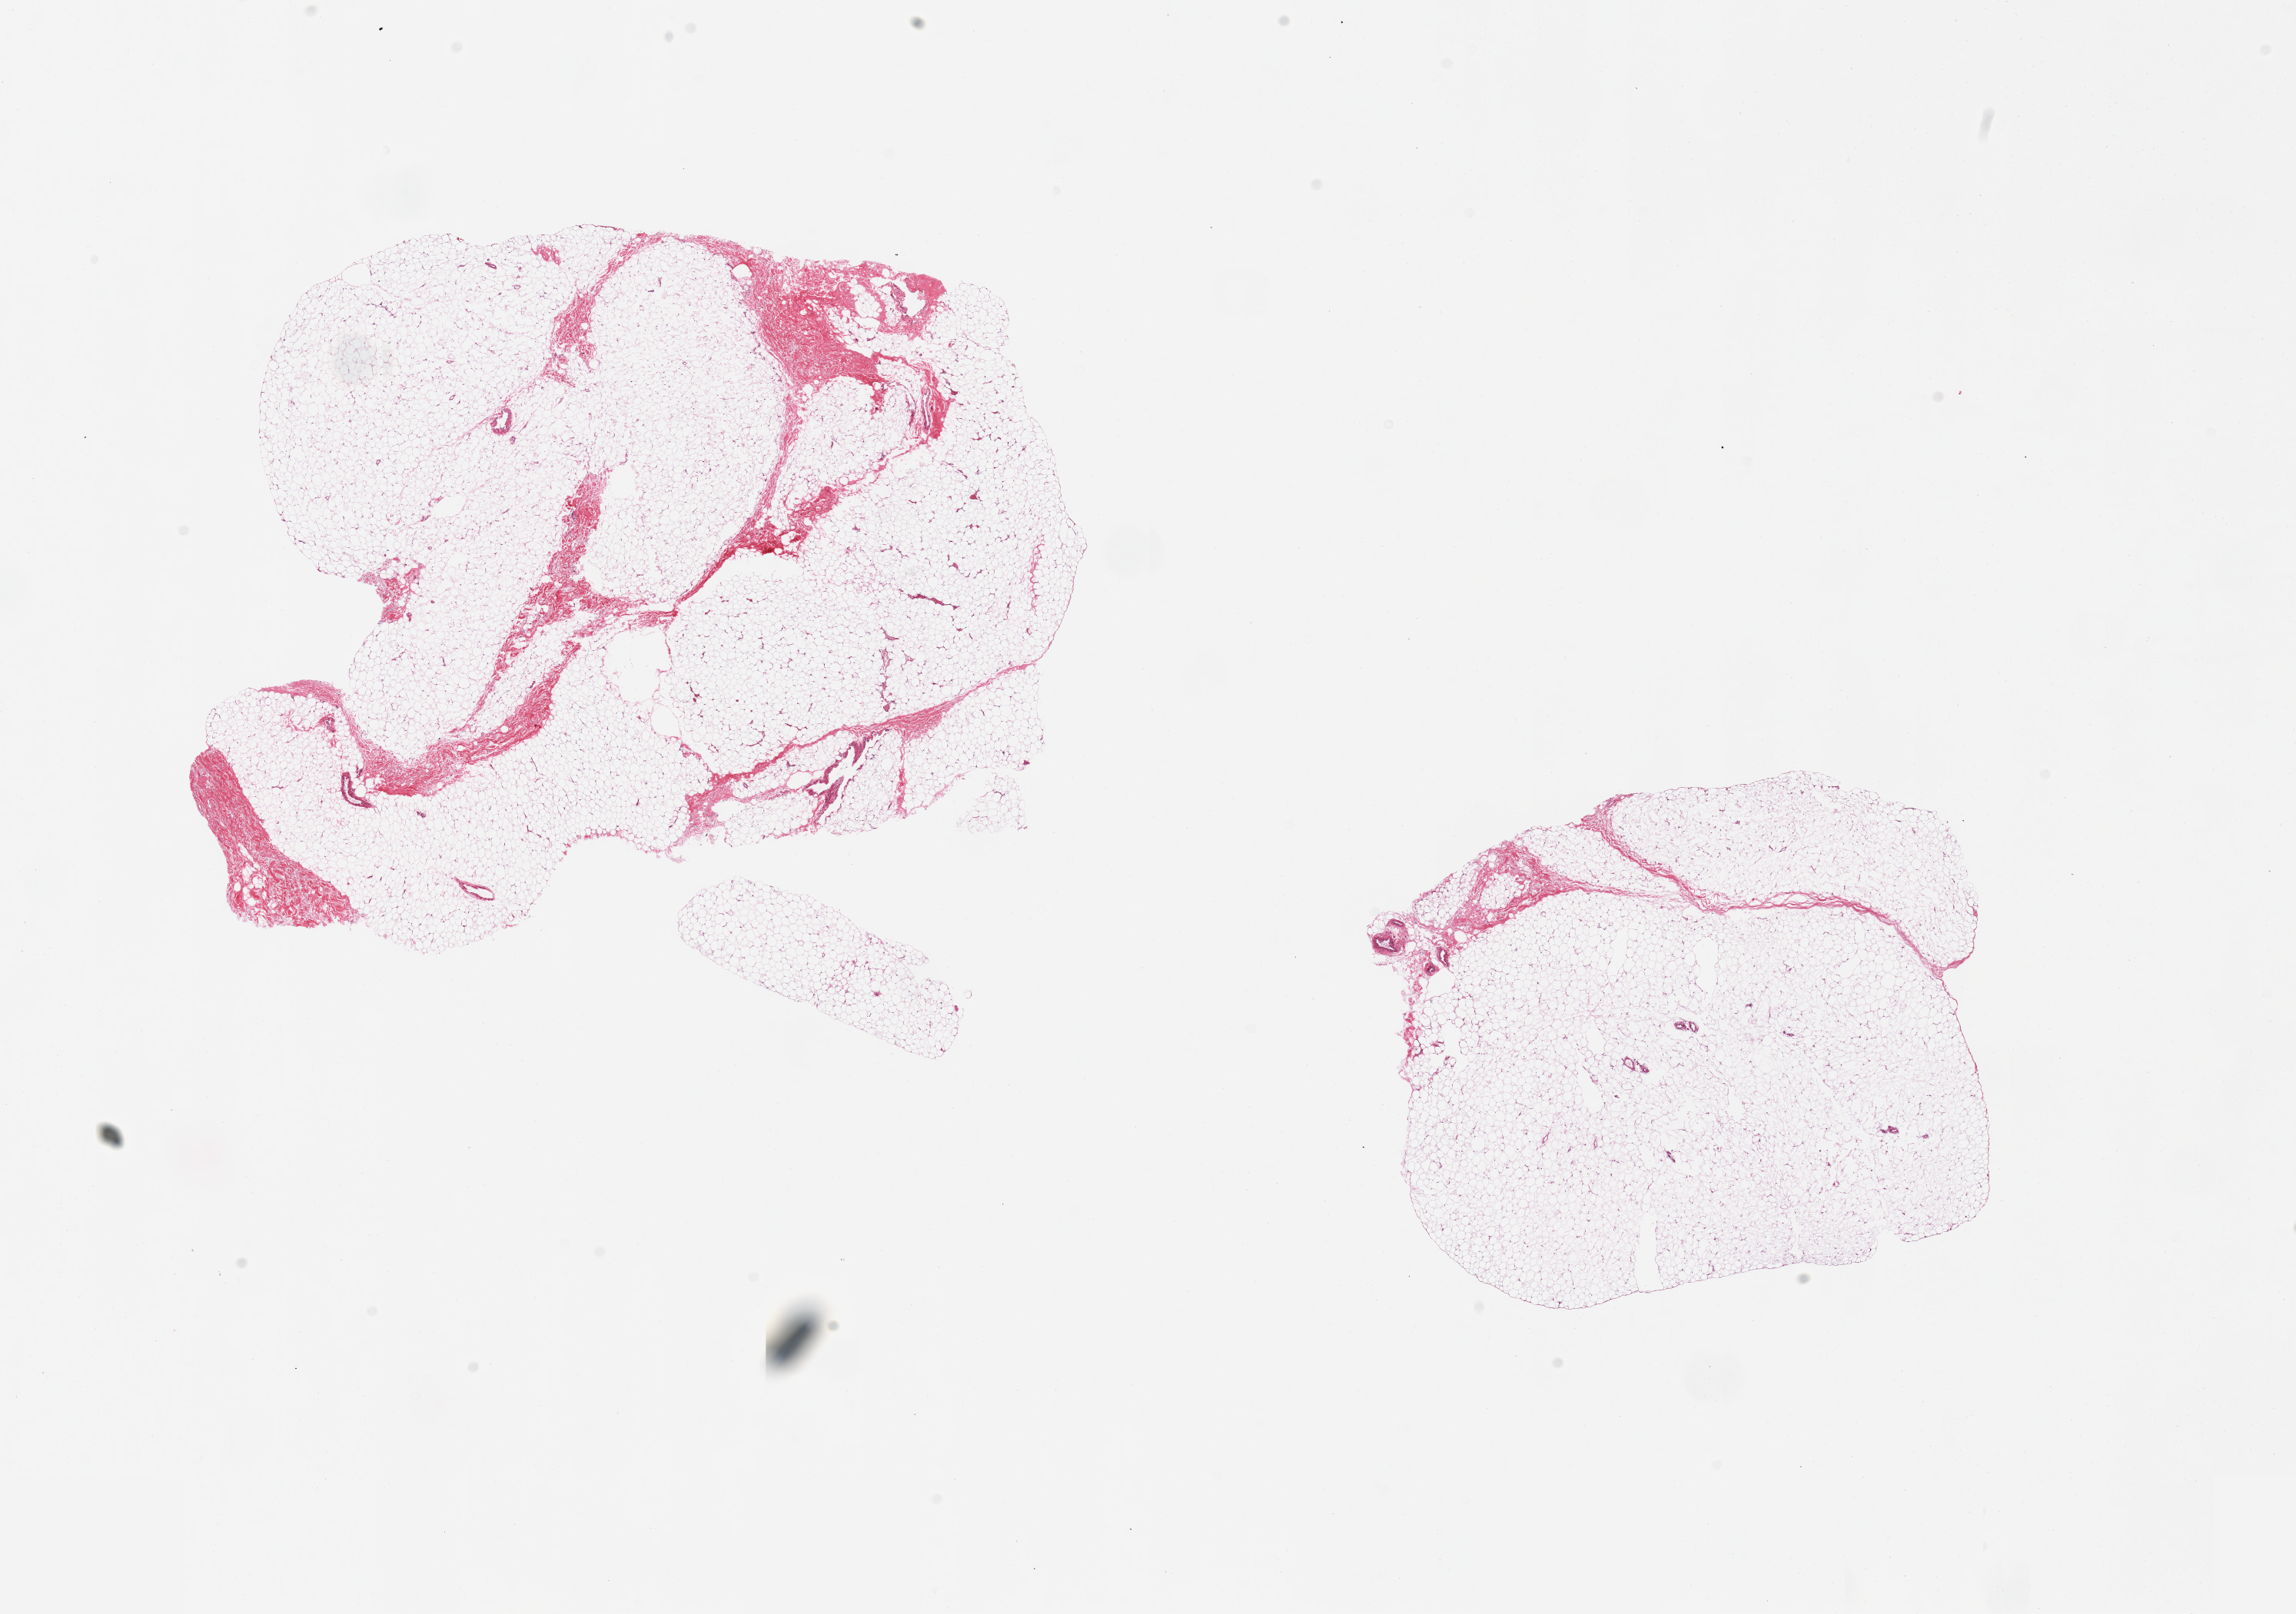
H&E whole-slide image, brightfield, low-resolution overview of the scanned area, about 23.6 x 16.6 mm (acquisition: 20x scan); PAXgene-fixed paraffin-embedded (PFPE) section; target tissue: breast; donor tissue sample. Donor sex: female.
Pathologist's review note for this sample: 2 pieces, fat only.